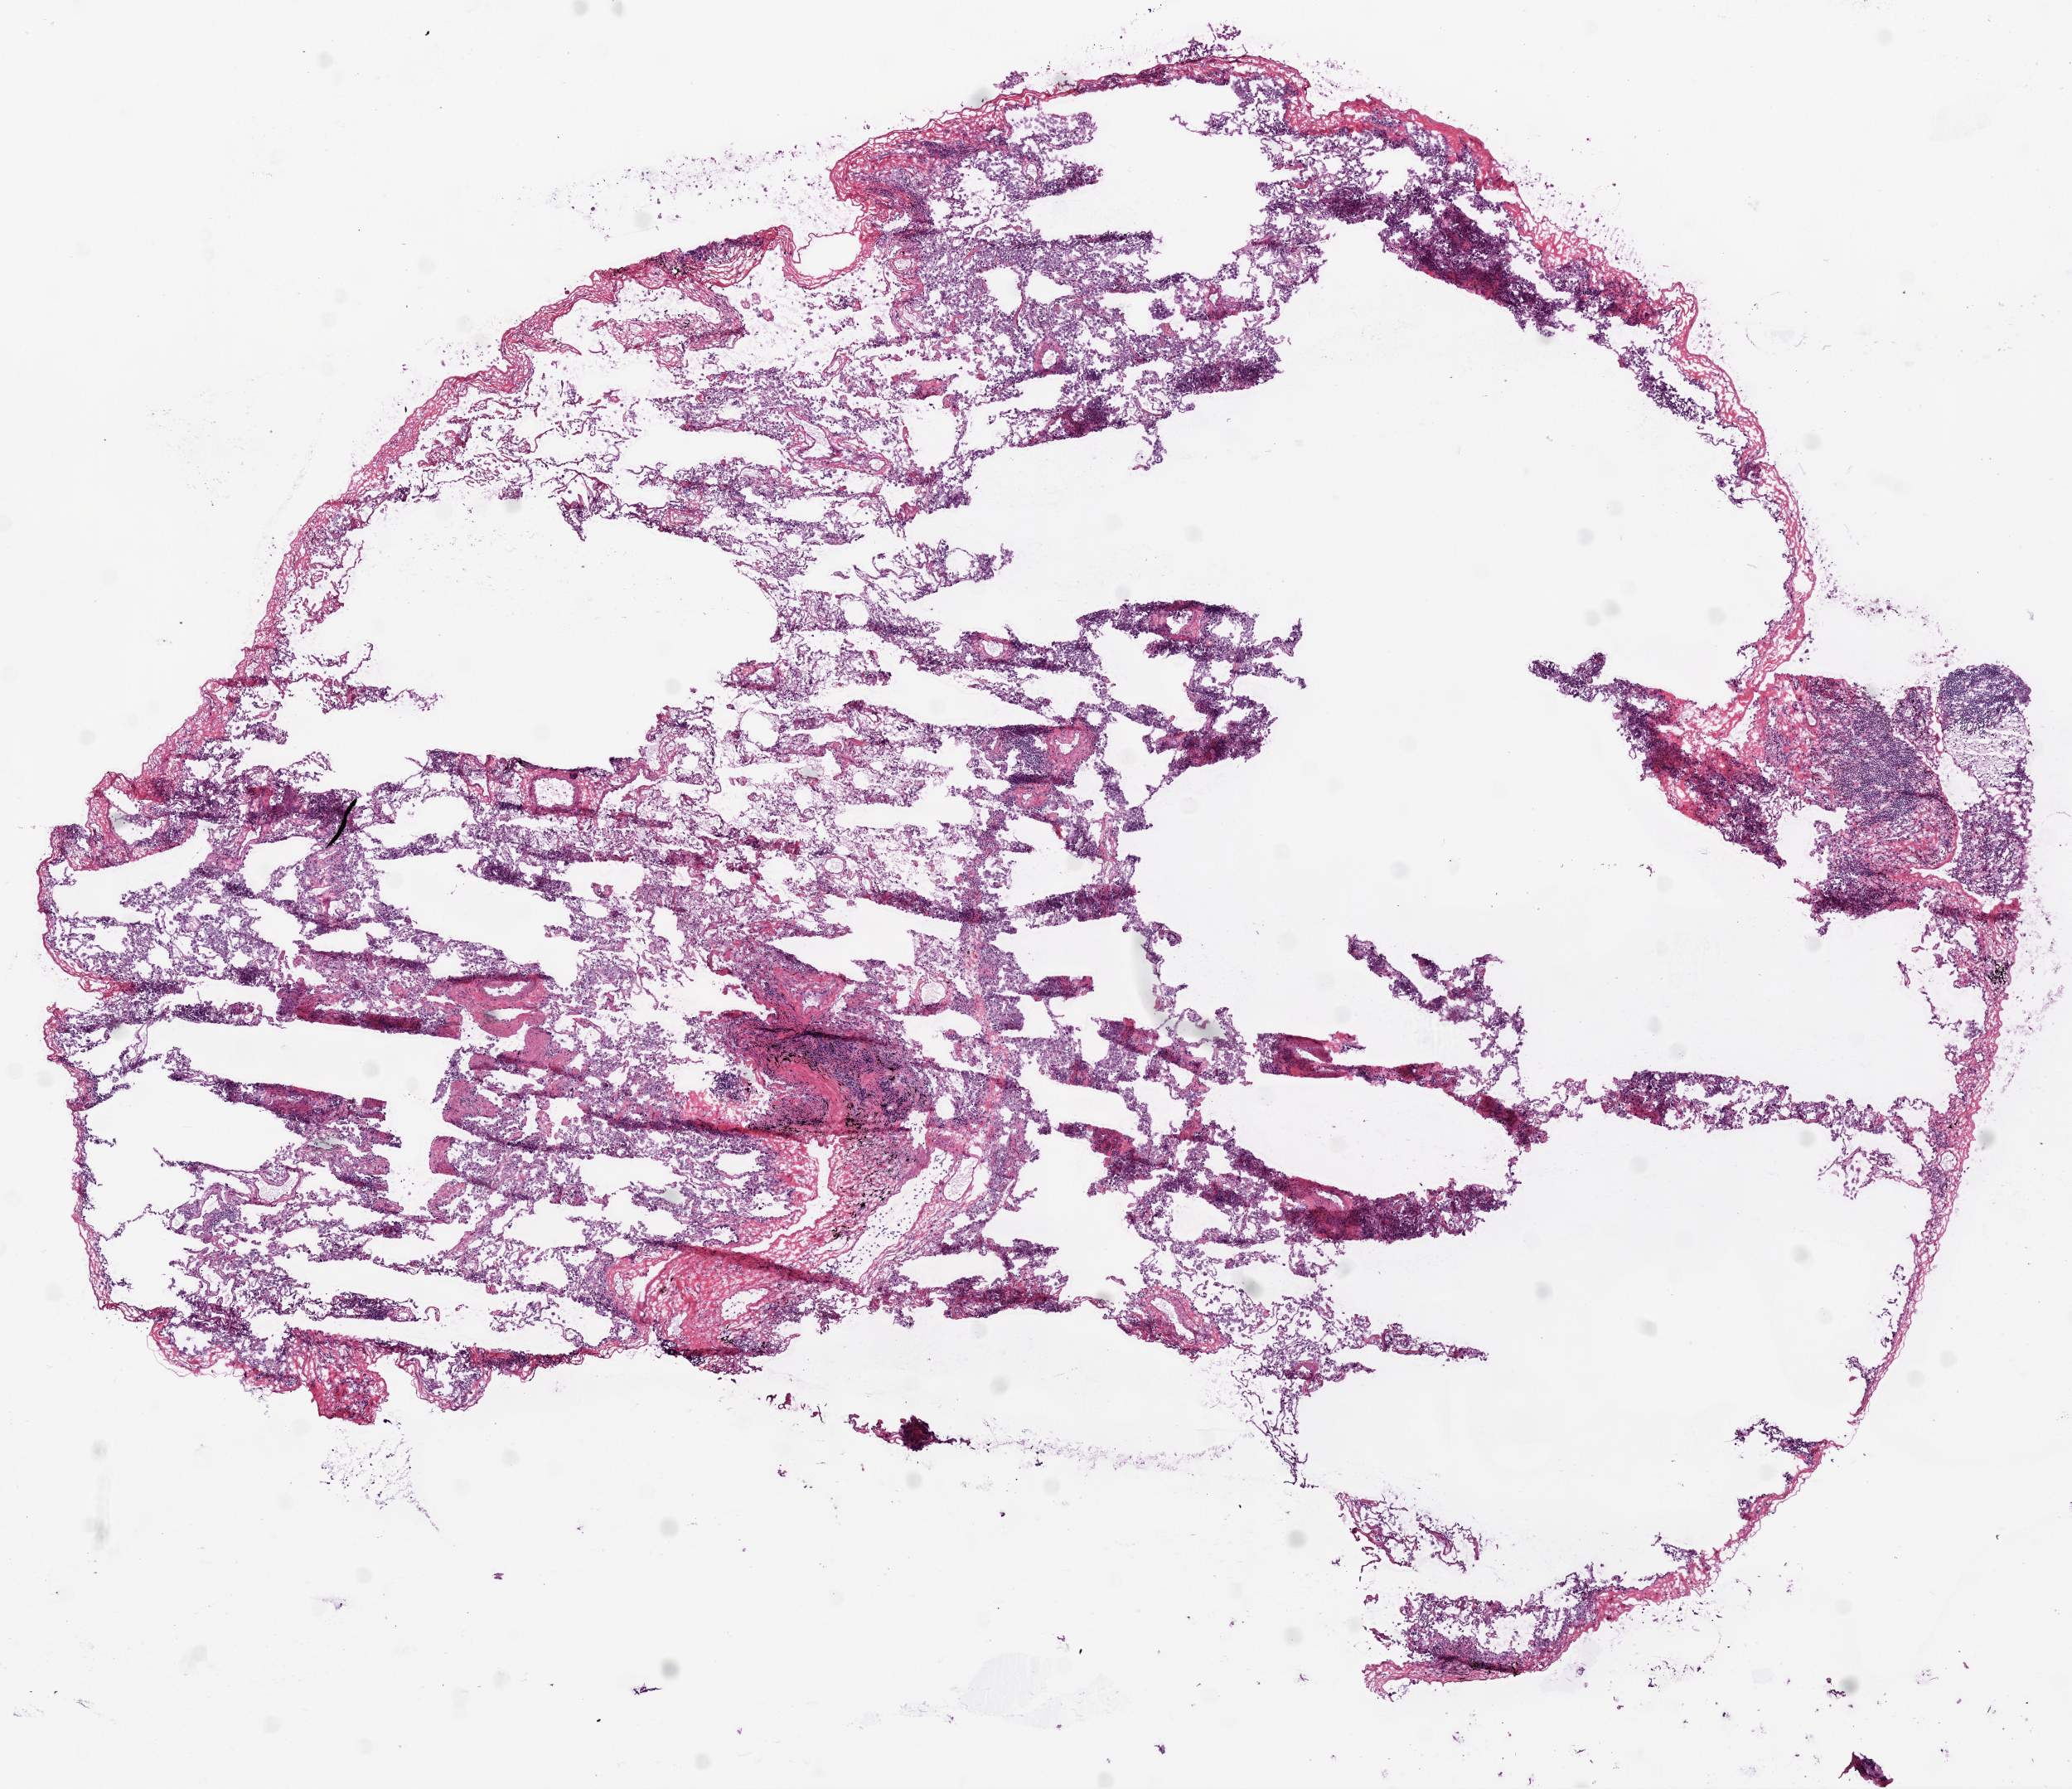
Digitized H&E-stained tissue section (whole slide), shown as a low-resolution overview of the whole scanned area (about 10.0 x 8.7 mm), frozen section from the bottom of the tissue portion, solid tissue normal (non-tumour tissue) sample from the lung. Male, age 60 years at initial diagnosis.
This section: solid tissue normal sample (biorepository sample class). Patient diagnosis: Squamous cell carcinoma, NOS (upper lobe, lung).